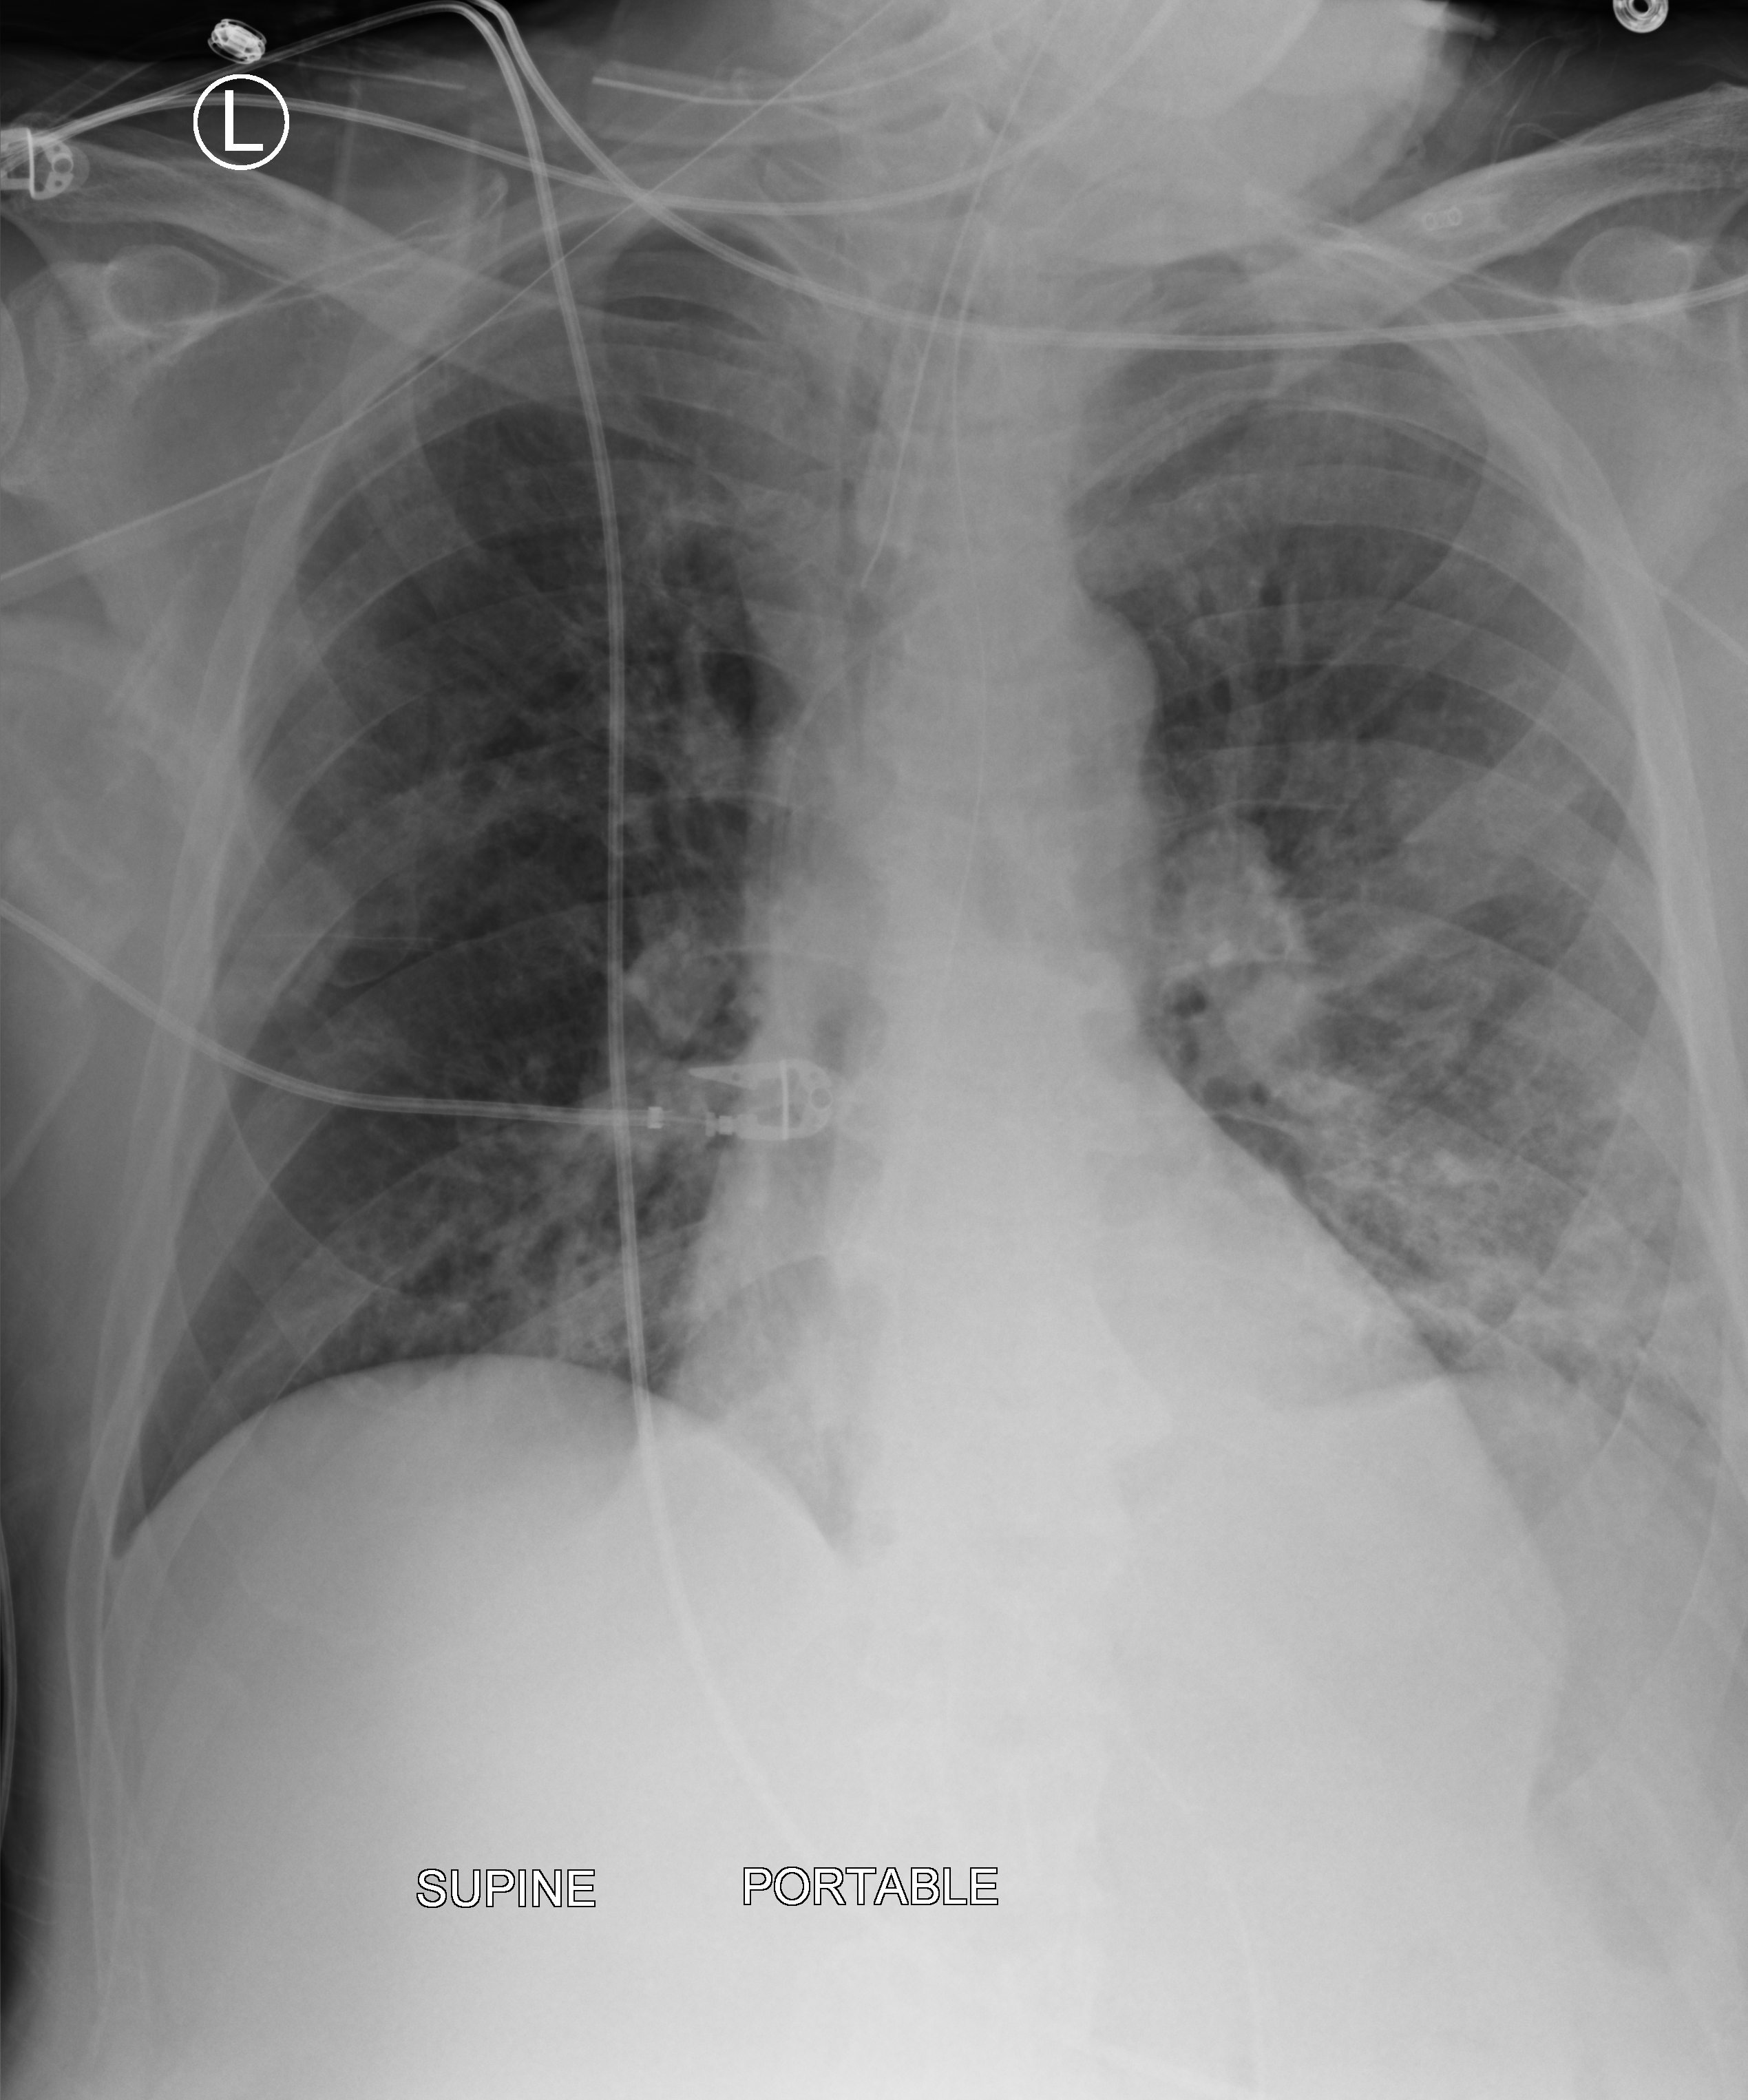
Bedside chest radiograph (computed radiography), anteroposterior (AP) projection. Male patient hospitalised with COVID-19, age 60–74 years.
Hospital-stay facts (about this admission, not read from this image; timing relative to this image not recorded): admitted to intensive care during this hospital stay: yes; length of hospital stay: 35 days.